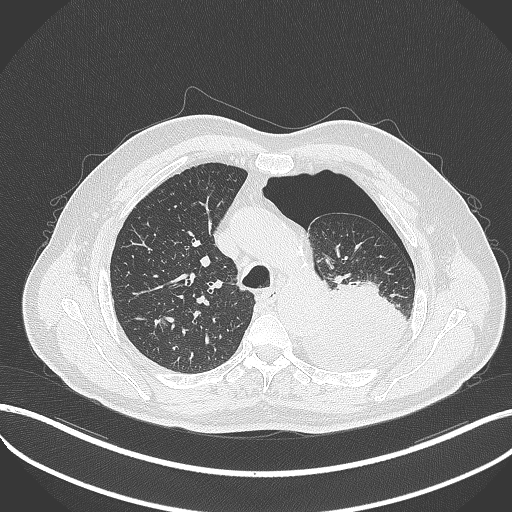
Chest CT, one axial slice; position 370 of 464 along the scan axis; reconstruction kernel B70f; 120 kVp; lung window (W 1500 / L -600 HU); 1 mm slice thickness; 512 × 512 image matrix. Male patient, age 76 years. Case-level facts recorded for this patient, not image findings: clinical TNM (as recorded): T3 N0 M1b.
Annotated regions visible in this slice (rectangle marked by the reading radiologist):
- lung tumour (recorded histology: adenocarcinoma): box from (x=297, y=282) to (x=408, y=374) px